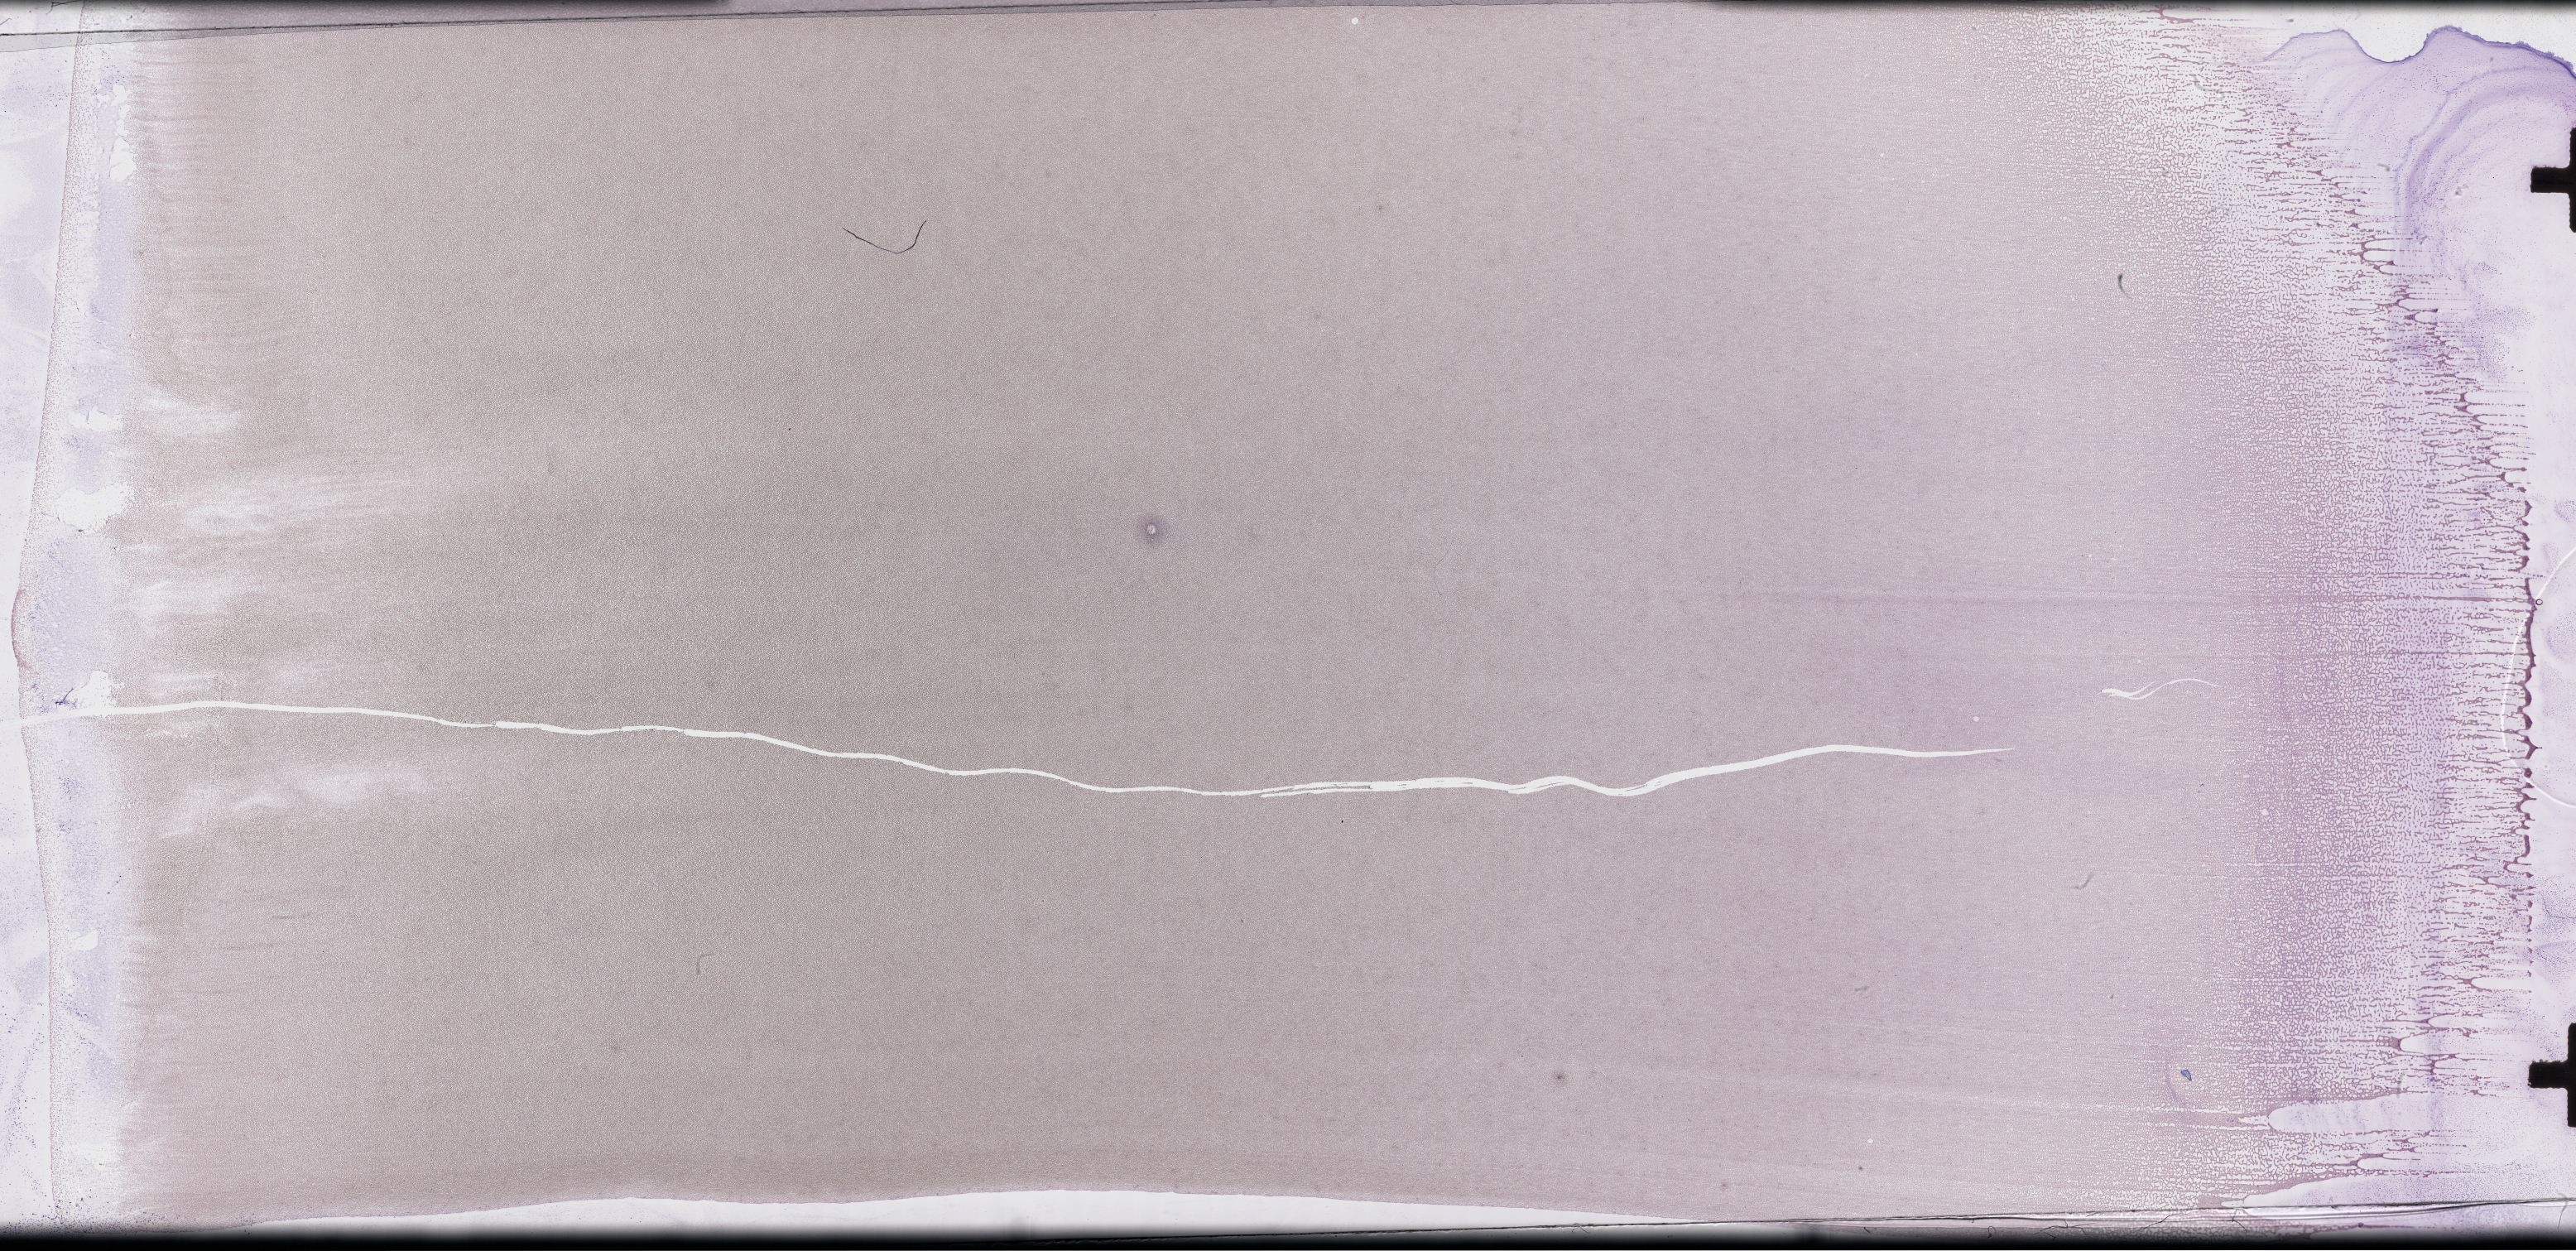
Wright-Giemsa-stained whole blood smear, whole-slide image — low-resolution overview of the scanned area, about 50.3 x 24.4 mm. Collected on treatment. Patient: male.
- from a patient with: Plasma Cell Myeloma